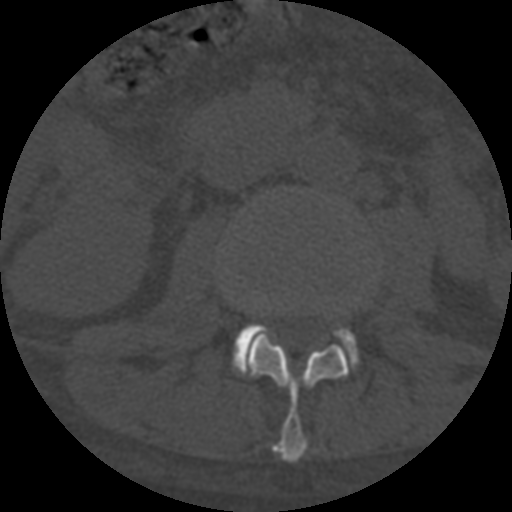
CT including the spine, one axial slice. Position 248 of 708 along the scan axis. 120 kVp. One of 3 acquisitions stored at this slice position. Bone window (W 1800 / L 400 HU). 512 × 512 image matrix, field of view 160 × 160 mm. Patient age 55 years. Case-level facts recorded for this patient, not image findings: primary cancer: colon.
Outlined on this slice (semi-automatic segmentation, software-assisted and operator-edited):
- L2 vertebra: box from (x=244, y=336) to (x=349, y=463) px
- L3 vertebra: (x=234, y=324)–(x=357, y=372)